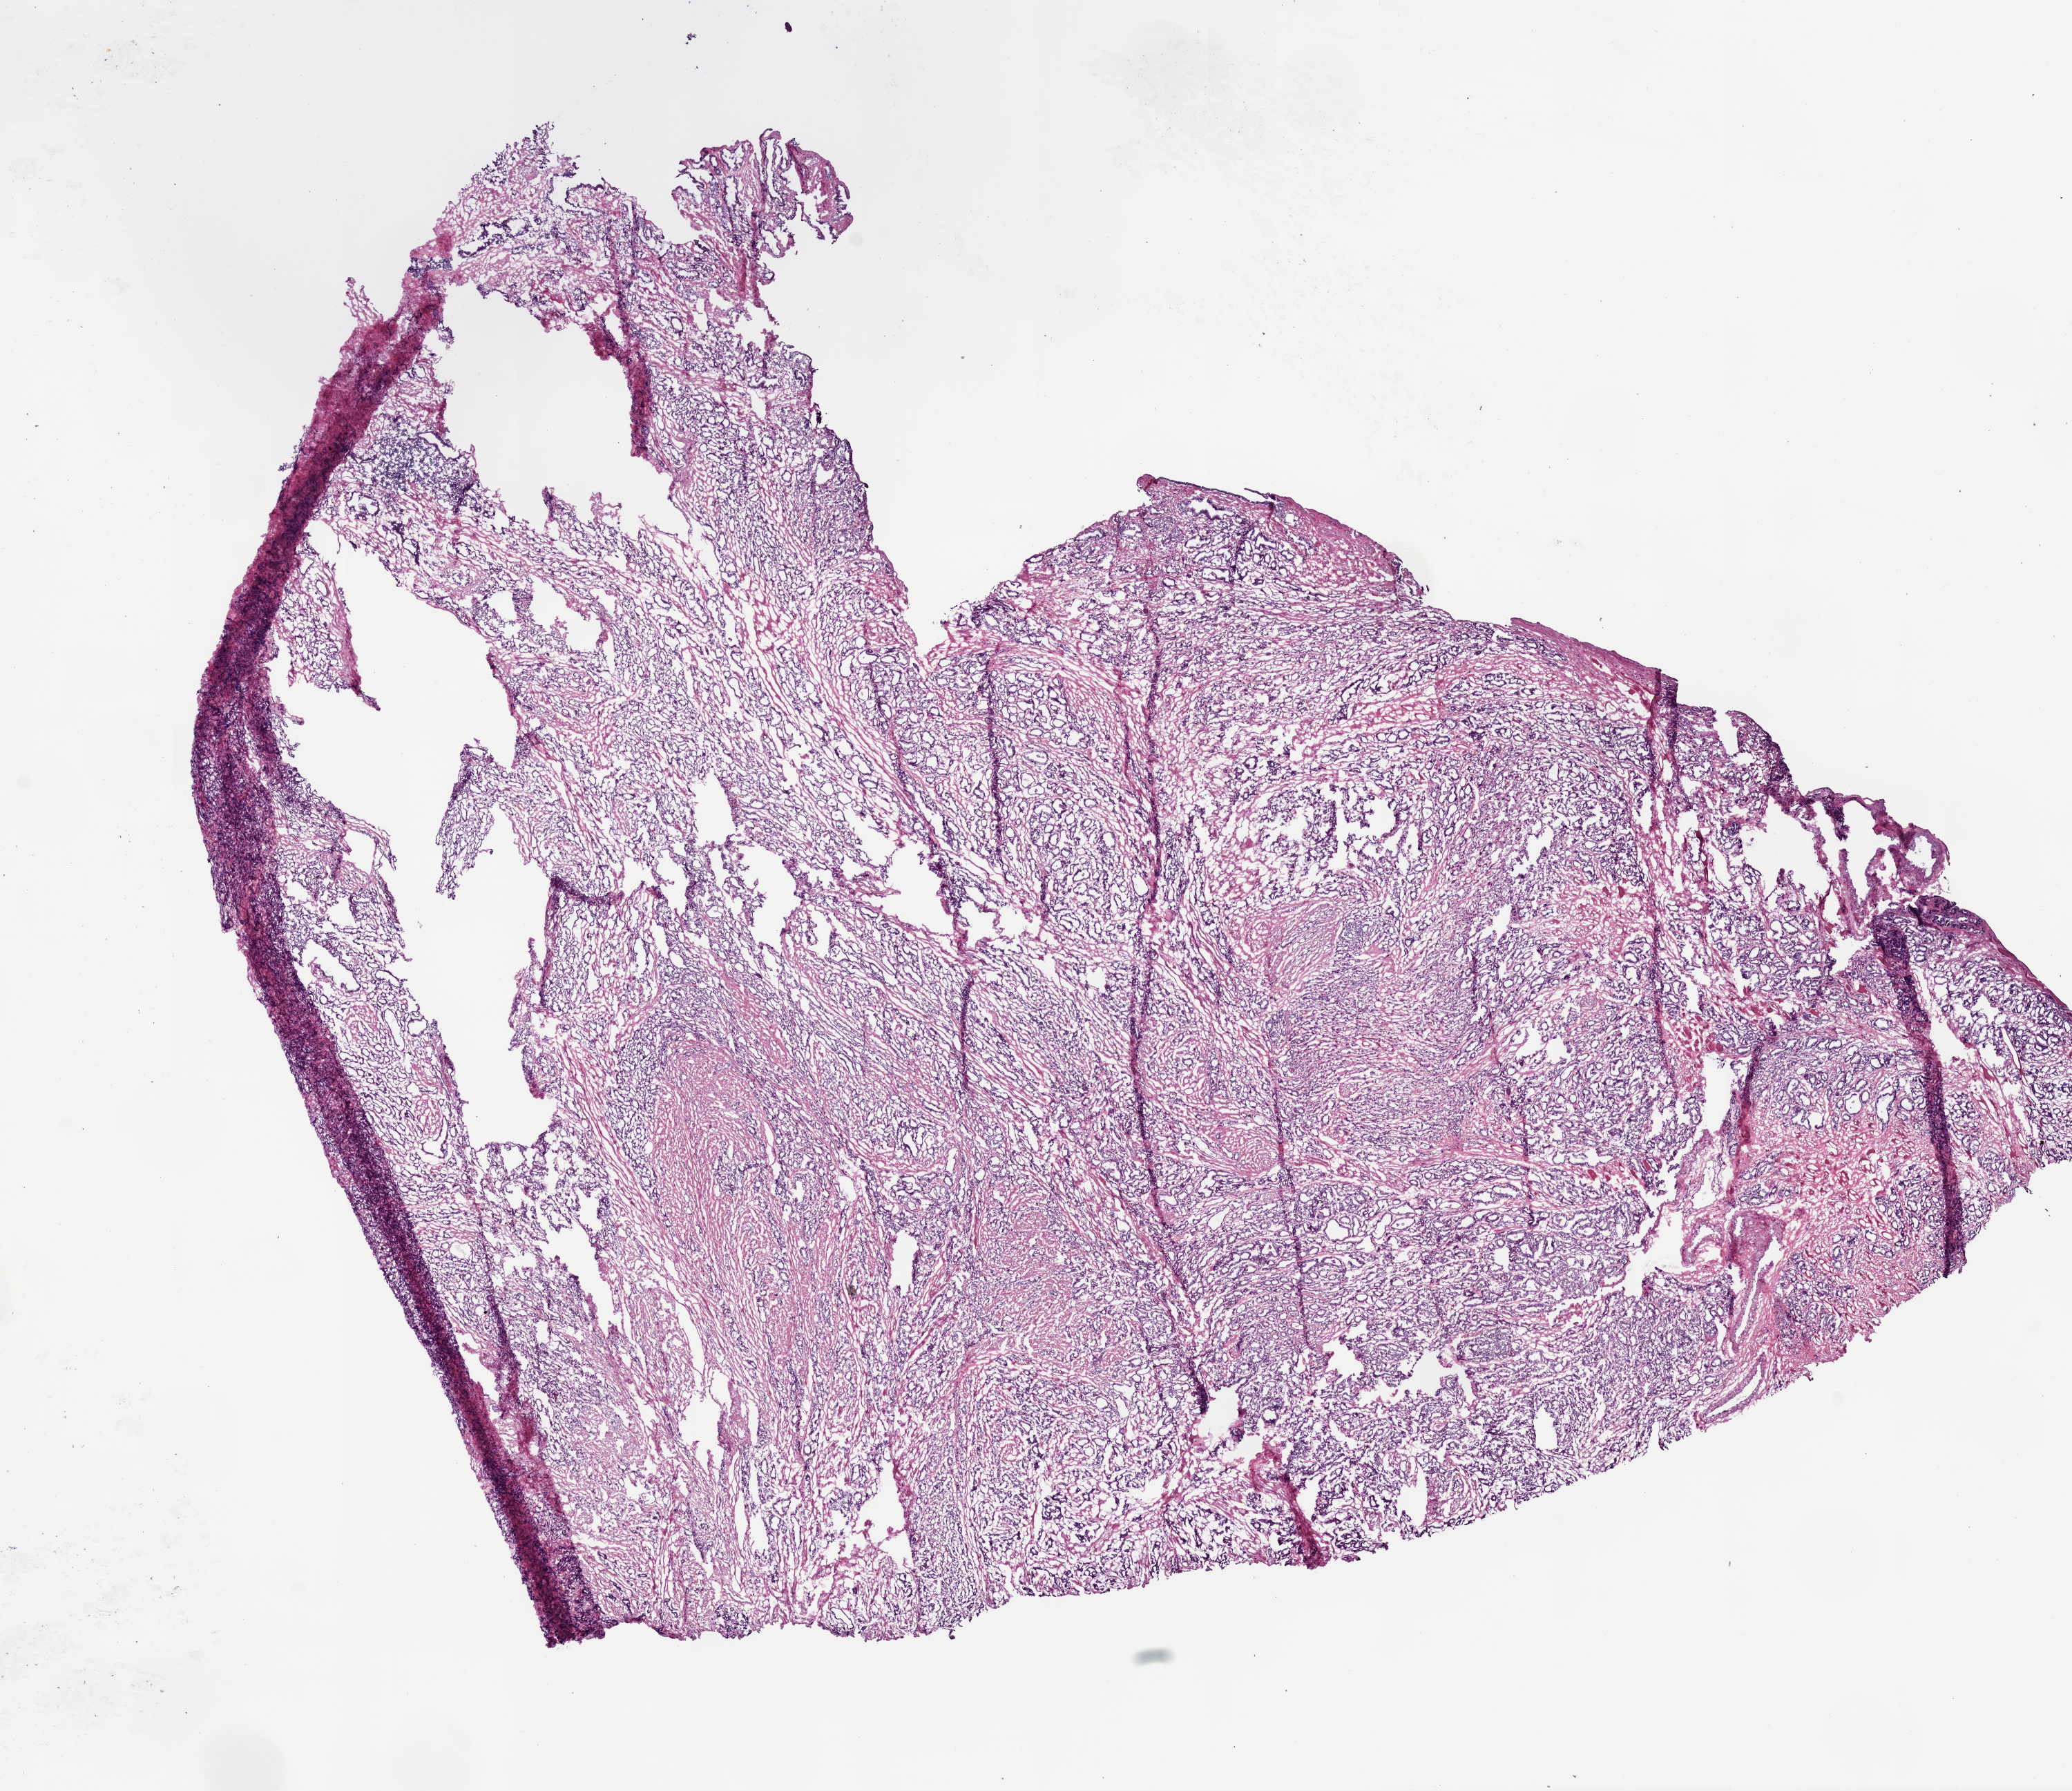
H&E-stained whole-slide image, shown as a low-resolution overview of the whole scanned area (about 12.0 x 10.4 mm). Frozen section from the bottom of the tissue portion. Primary tumour sample from the prostate. Male patient; age at initial diagnosis 50 years. Gleason score: 7 (4+3). Composition of this section per pathologist review: tumour cells 80%, tumour nuclei 85%, normal cells 2%, stromal cells 18%, necrosis 0%. Infiltration values recorded for this section: lymphocyte infiltration 0%, monocyte infiltration 0%, neutrophil infiltration 0%.
* pathologic diagnosis: Acinar cell carcinoma (prostate gland)